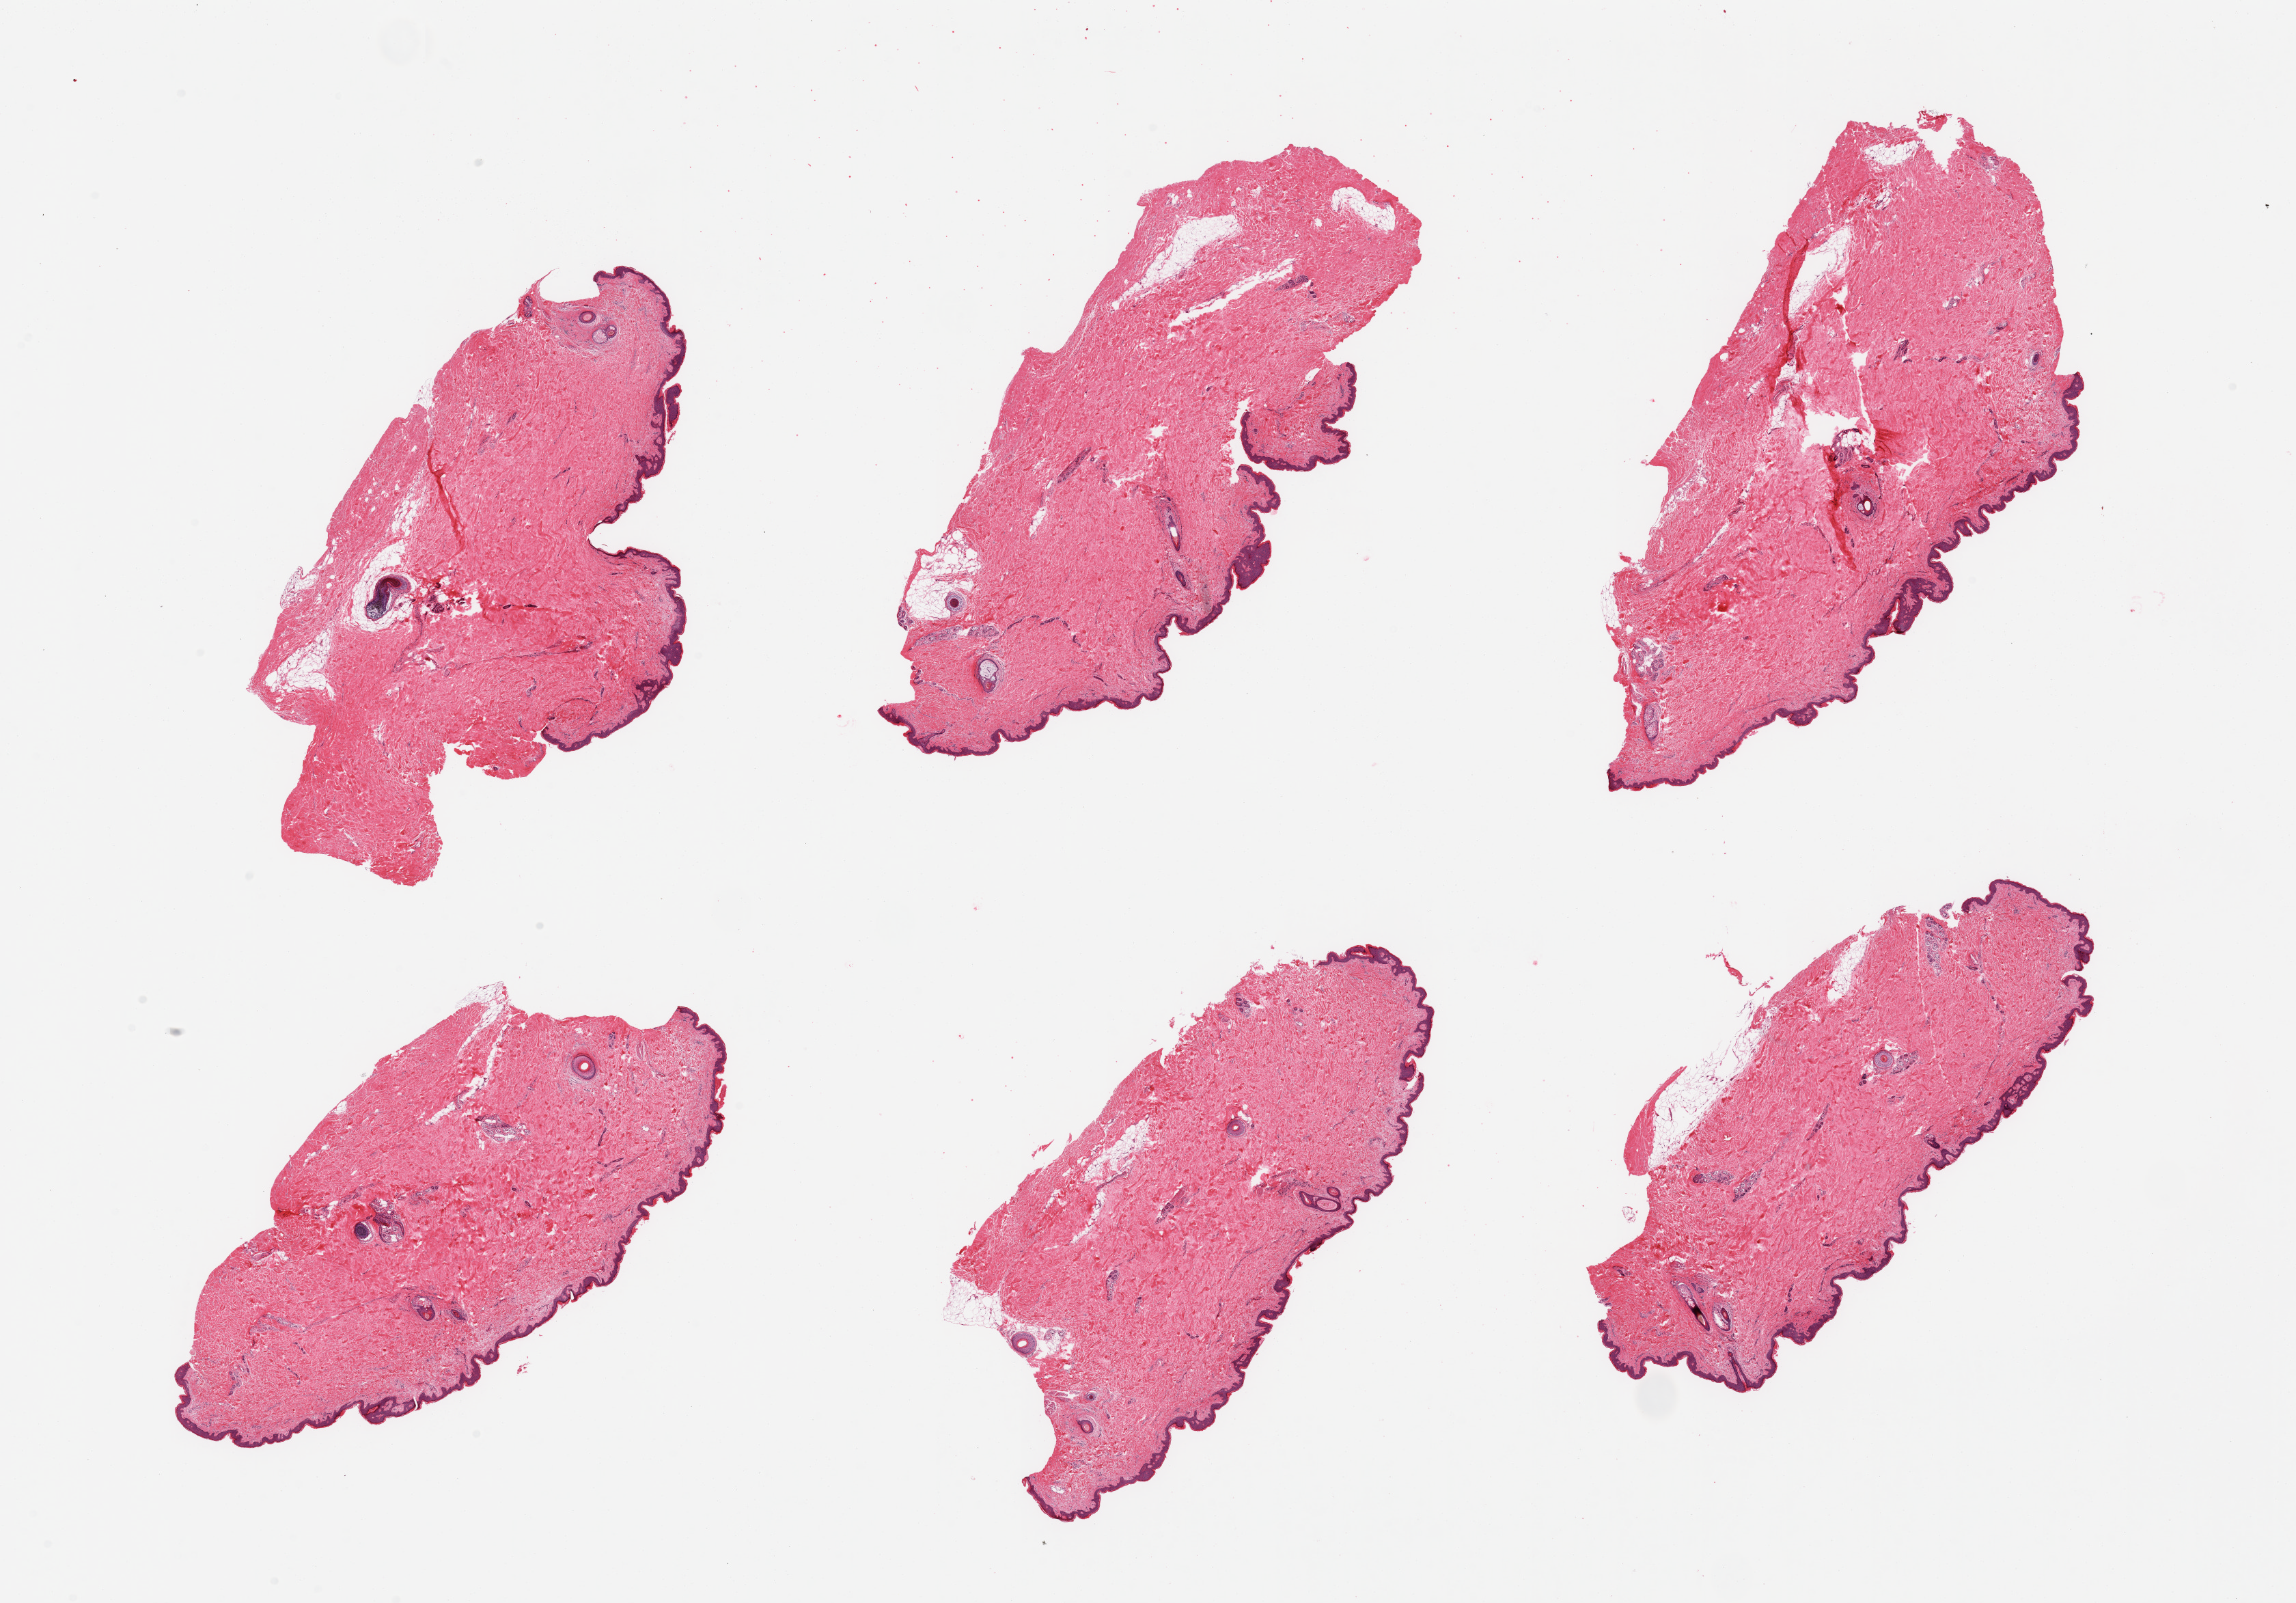
H&E whole-slide image, whole scanned area (about 26.6 x 18.6 mm, slide scanned at 20x) shown as a low-resolution overview. PAXgene-fixed paraffin-embedded (PFPE) section. Section of skin of suprapubic region (target tissue). Tissue donor sample. Donor: male.
Pathologist's review note for this sample: 6 pieces, minimal dermal fat; squamous epithelium is ~50 microns.